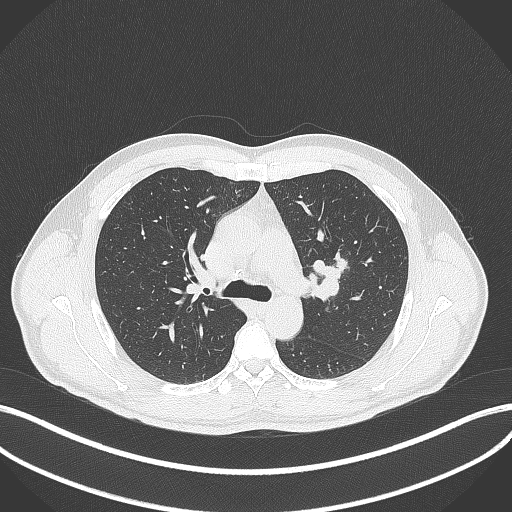
Chest CT, one axial slice. Slice 278 of 392 in the series (ordered by position). Reconstruction kernel B70f. Lung window (W 1500 / L -600 HU). 512 × 512 image matrix, field of view 400 × 400 mm. Male patient, age 50 years. Case-level facts recorded for this patient, not image findings: clinical TNM (as recorded): T1c N1 M1b.
Structures marked on this image (bounding box drawn by a radiologist):
- lung tumour (recorded histology: squamous cell carcinoma): box from (x=308, y=249) to (x=347, y=303) px